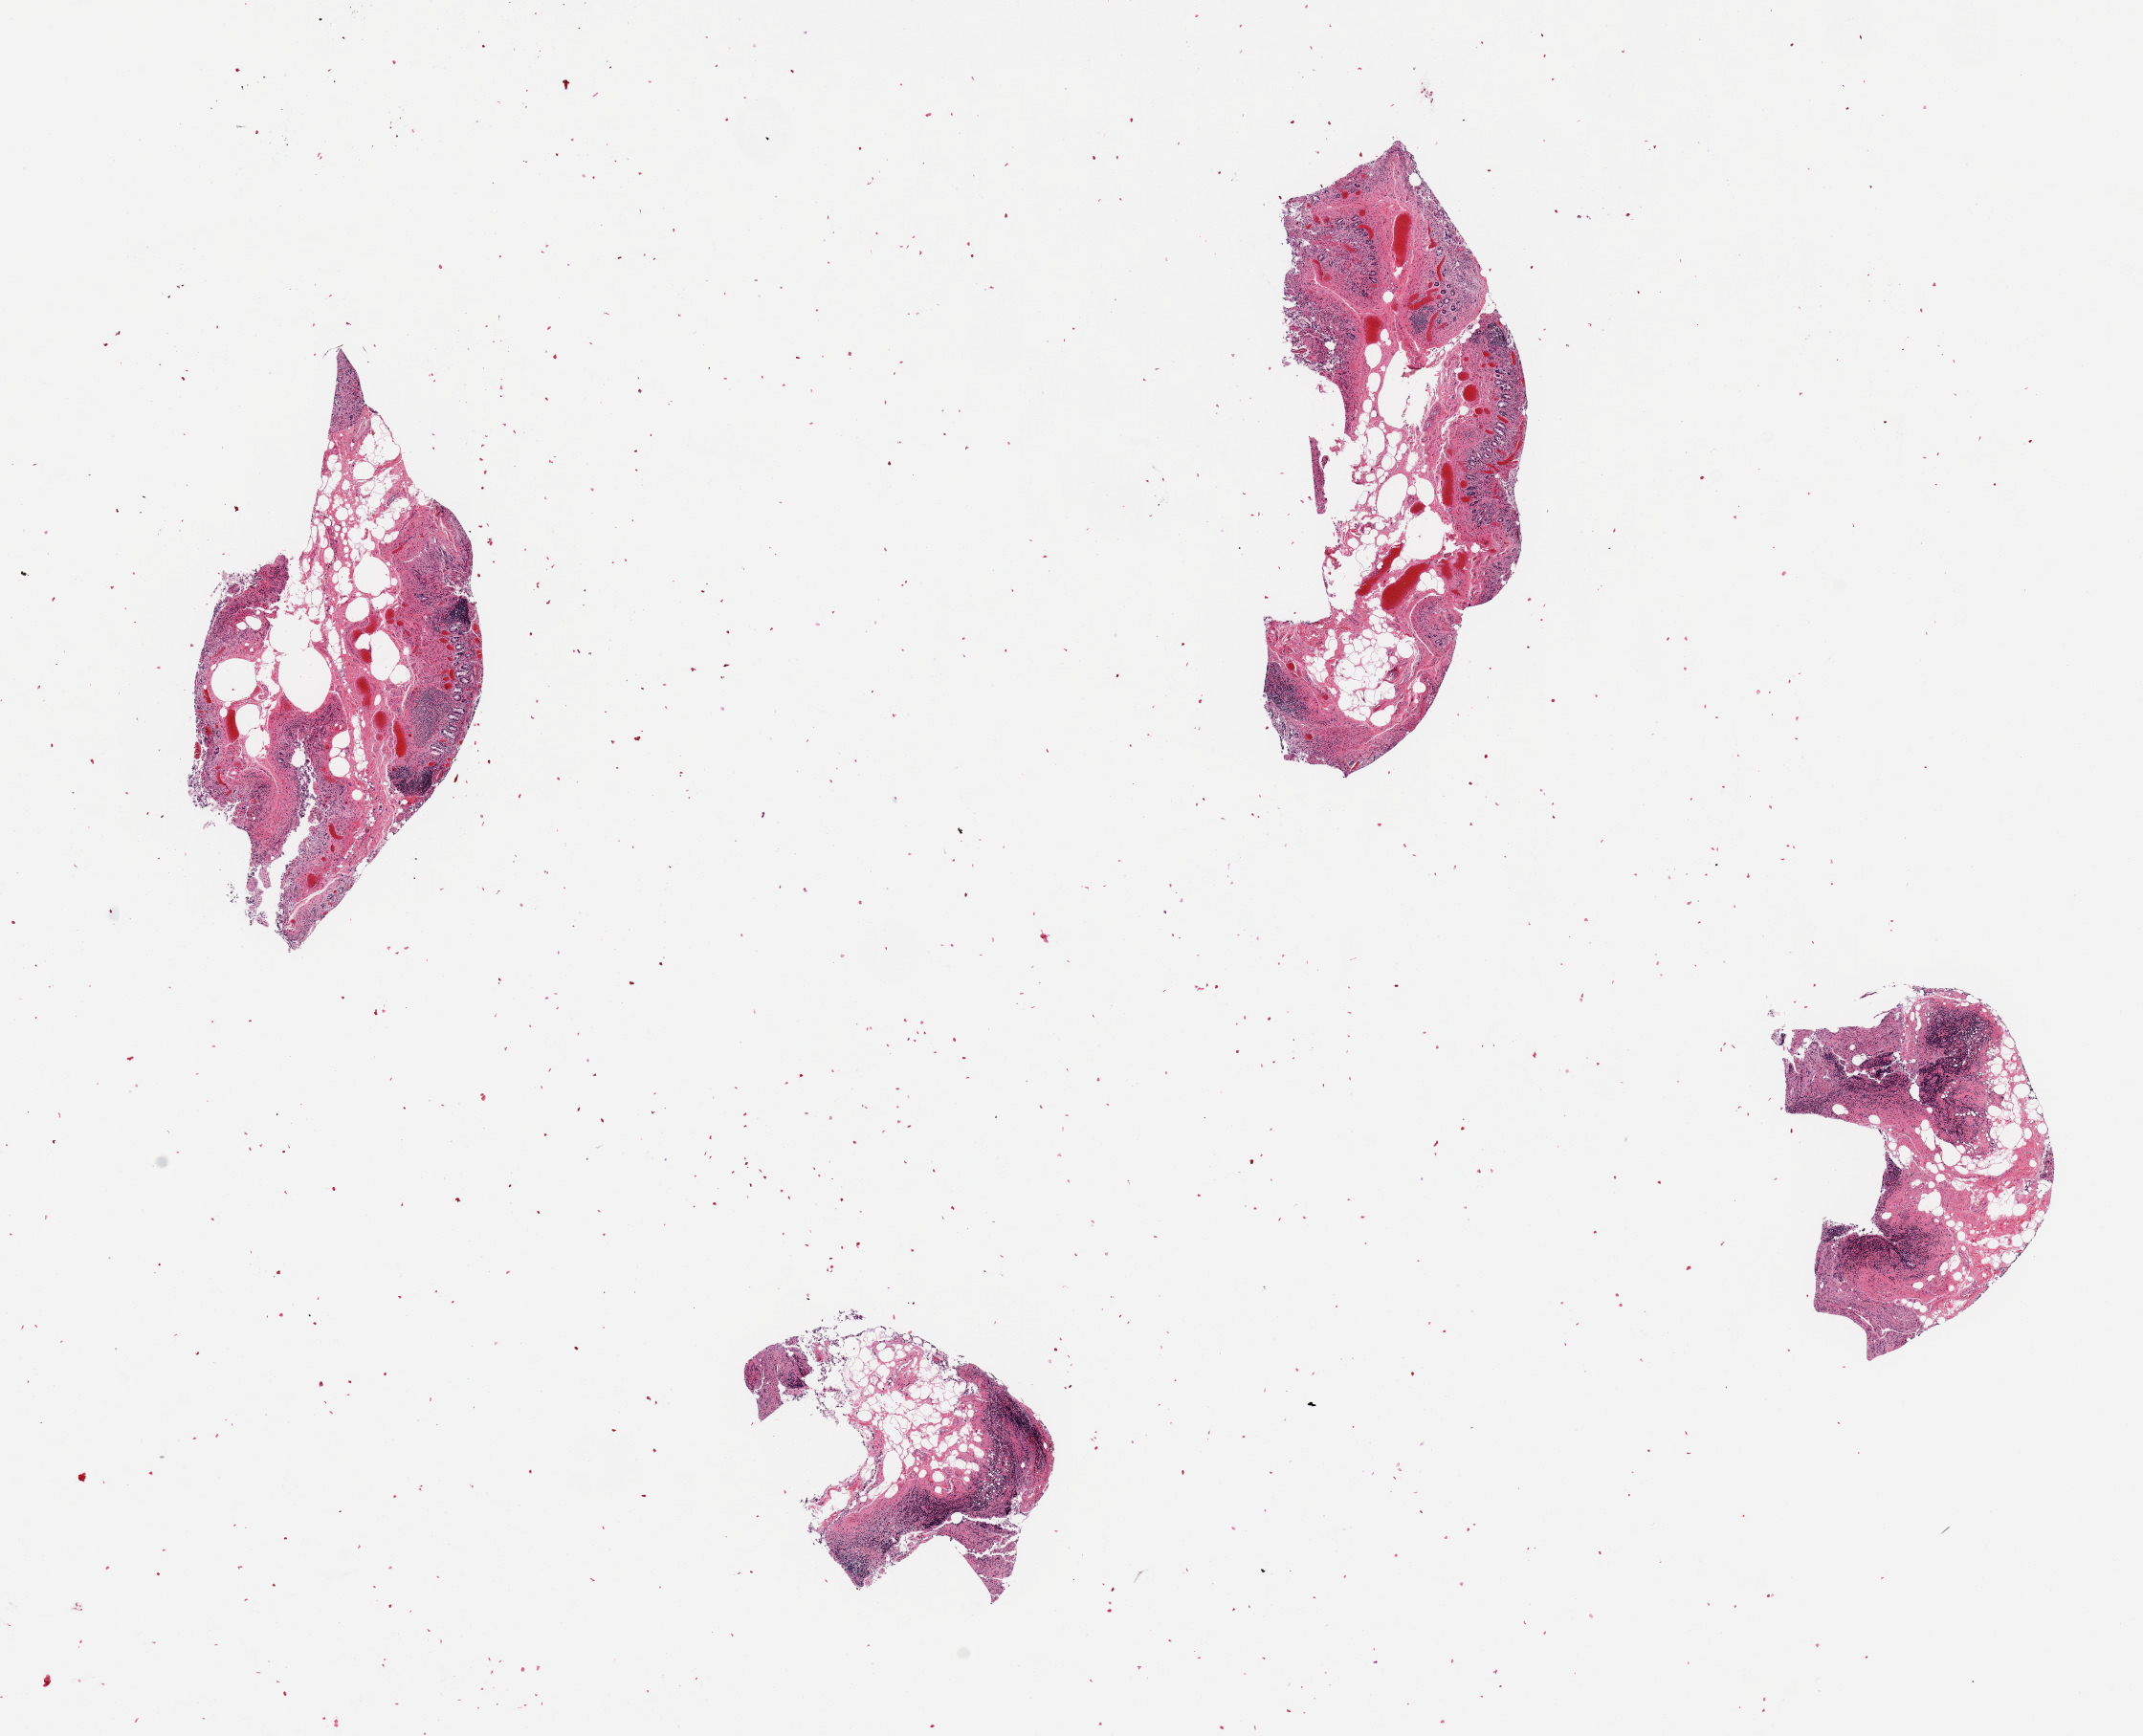
Hematoxylin and eosin (H&E) whole-slide image — whole scanned area (about 17.7 x 14.4 mm, from a 20x scan) shown as a low-resolution overview; PAXgene-fixed, paraffin-embedded tissue; target tissue: ileum; tissue donor sample. Male donor.
* pathologist's review note for this sample: 4 pieces, up to 5x2mm; ~10-20% lymphoid elements, poorly preserved